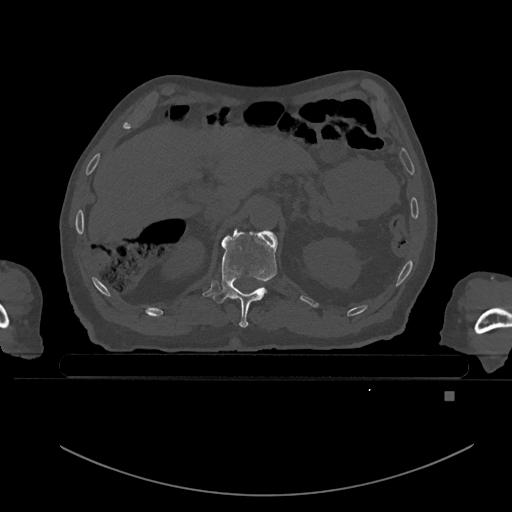
CT including the spine, one axial slice. Position 20 of 969 along the scan axis. Bone window (W 1800 / L 400 HU). 0.5 mm slice thickness. 512 × 512 image matrix, field of view 456 × 456 mm. Patient: male, 82 years. Case-level facts recorded for this patient, not image findings: primary cancer: prostate.
Outlined on this slice (semi-automatic segmentation, software-assisted and operator-edited):
- T11 vertebra: bounding box [x1, y1, x2, y2] px = [213, 231, 278, 328]